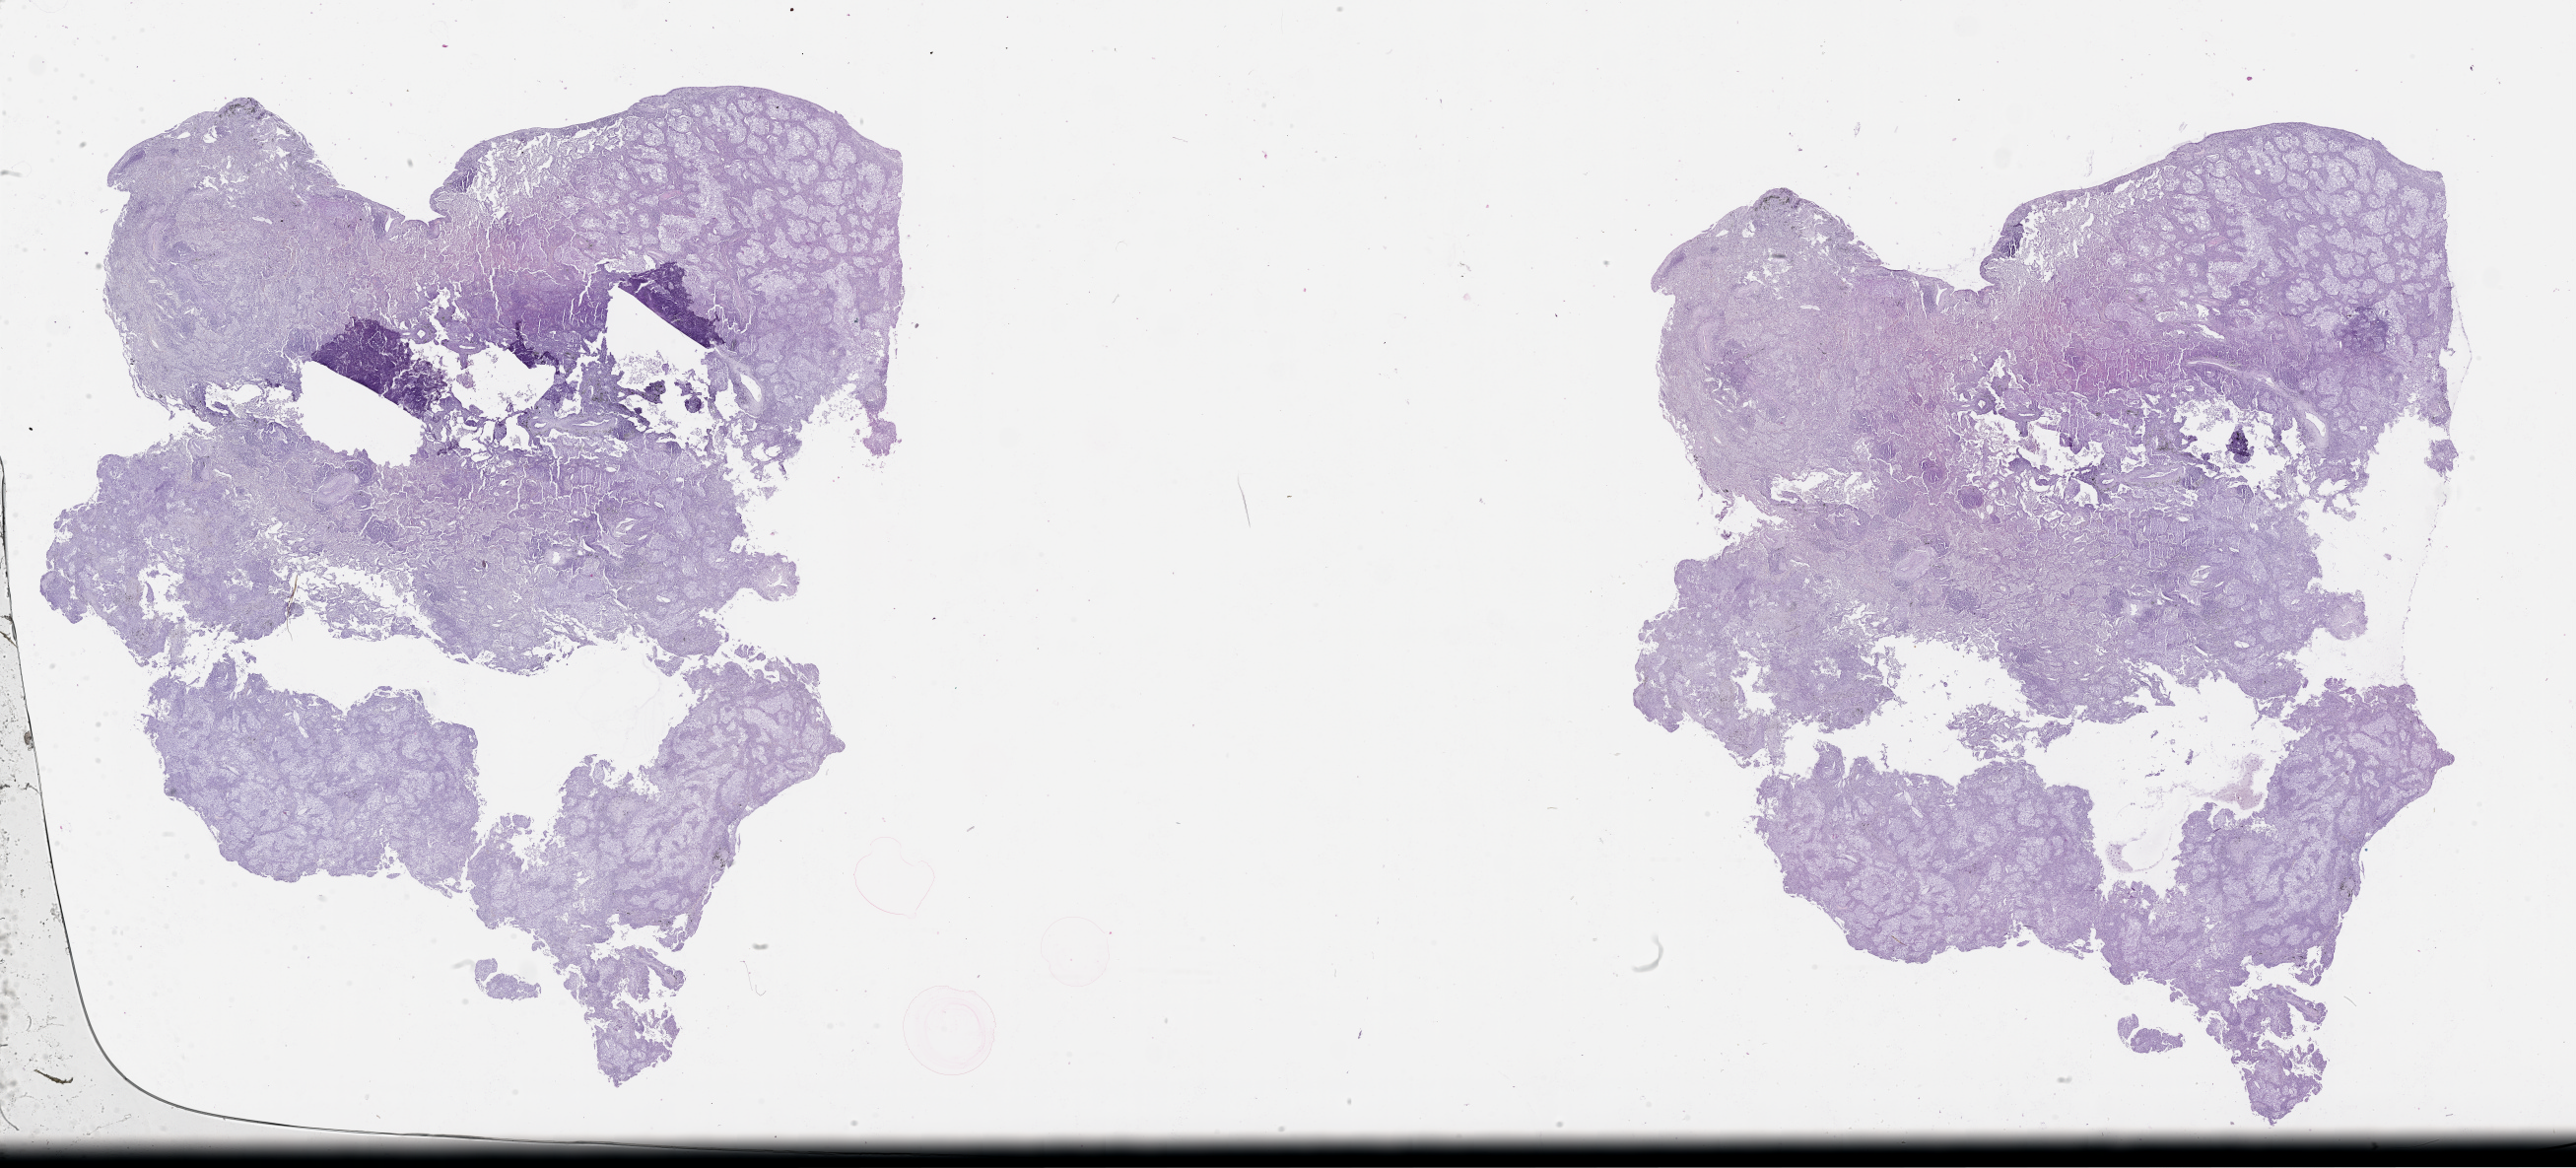
Whole-slide histology image, H&E — low-resolution overview of the scanned area, about 42.1 x 19.1 mm (from a 20x scan), tumour tissue sample, lung. Patient: male, age 68 years.
- patient diagnosis (cohort enrolment): squamous cell carcinoma (lung)